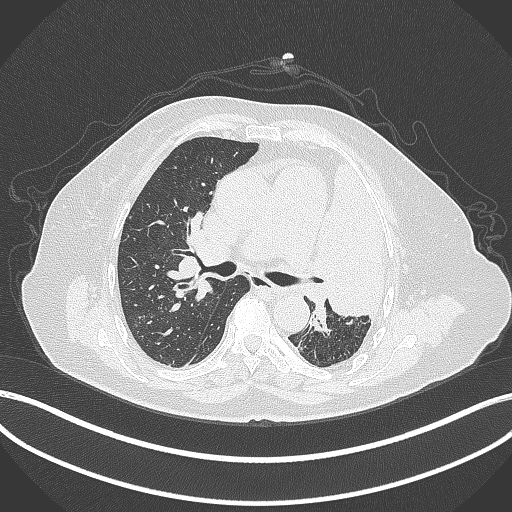
Chest CT, one axial slice; position 236 of 399 along the scan axis; reconstruction kernel B70f; lung window (W 1500 / L -600 HU); 1 mm slice thickness; 512 × 512 image matrix, field of view 400 × 400 mm. Patient: female, 75 years. From the clinical record (not read from this slice): clinical TNM (as recorded): T3 N3 M1.
Structures marked on this image (rectangle marked by the reading radiologist):
- lung tumour (recorded histology: adenocarcinoma): bounding box [x1, y1, x2, y2] px = [322, 155, 390, 325]